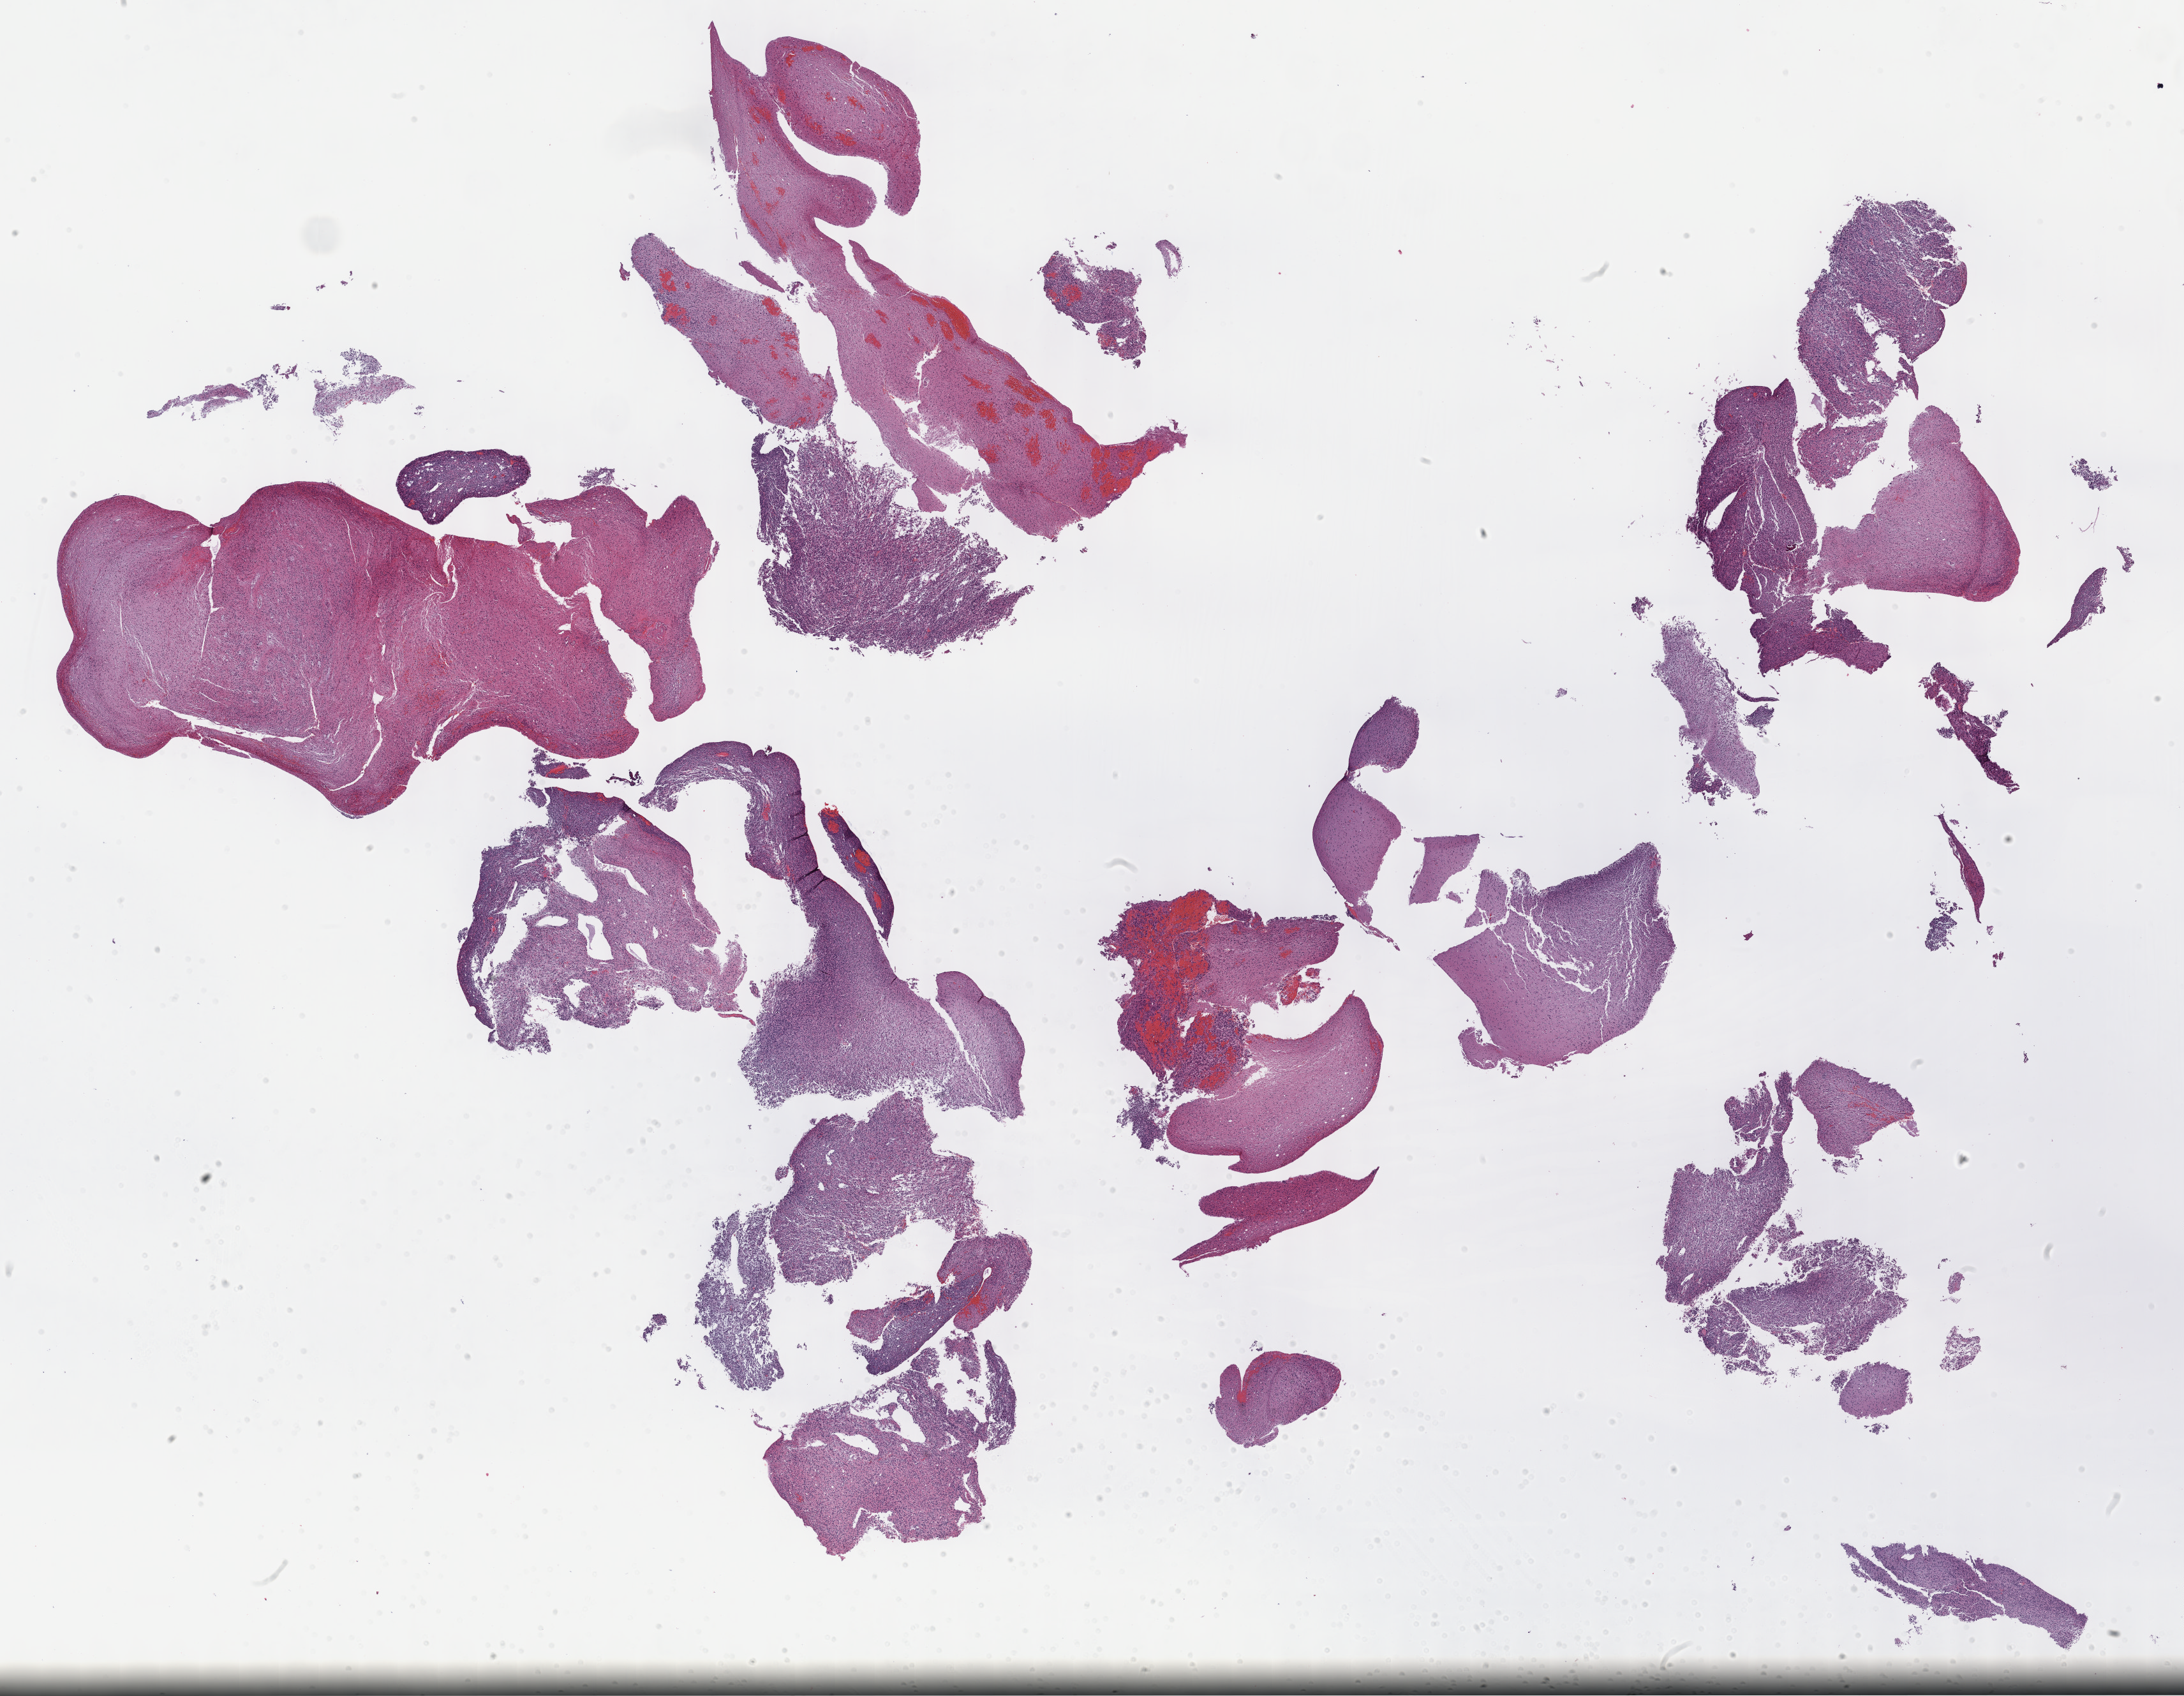
H&E whole-slide image, whole scanned area (about 27.7 x 21.5 mm, acquisition: 40x scan) shown as a low-resolution overview, formalin-fixed paraffin-embedded (FFPE) diagnostic section, brain, primary tumour sample. Female, age 44 years at initial diagnosis. Histologic grade: G3 (poorly differentiated).
• pathologic diagnosis: Astrocytoma, anaplastic (cerebrum)
• laterality: left